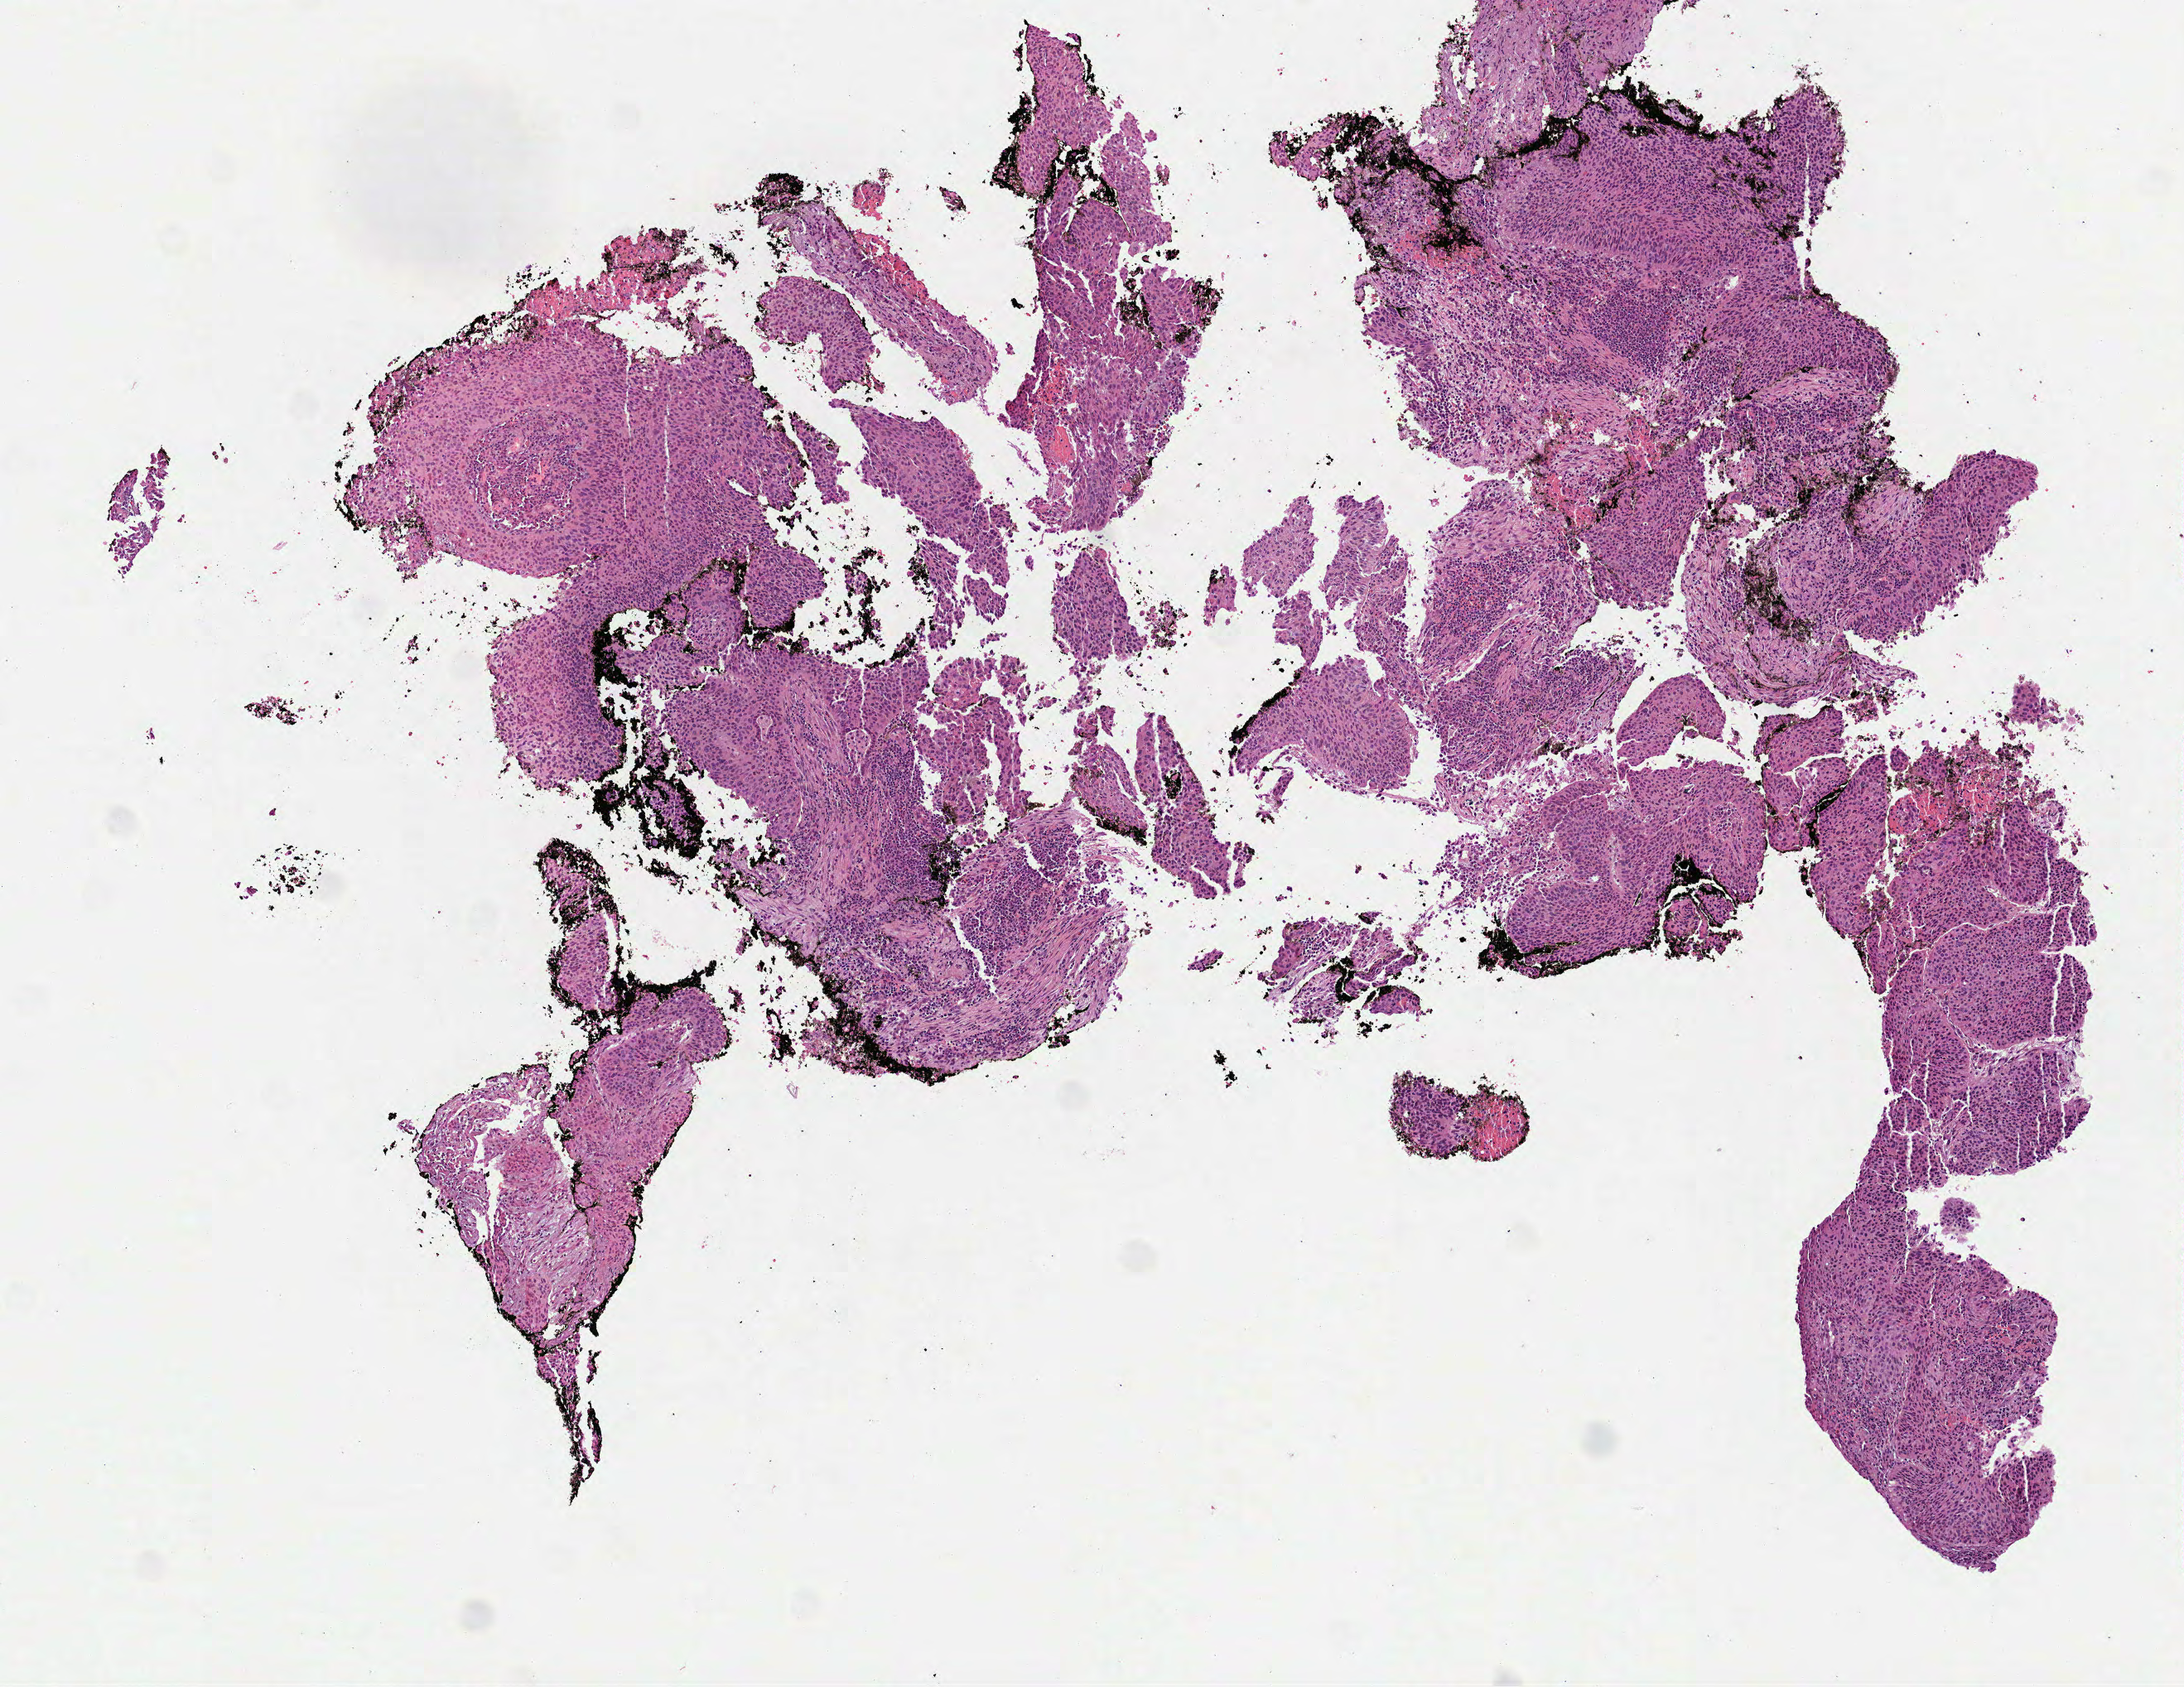
Digitized H&E tissue section (whole slide) — shown as a low-resolution overview of the whole scanned area (about 5.3 x 4.1 mm, from a 40x scan); formalin-fixed paraffin-embedded (FFPE) diagnostic section; lung, primary tumour sample. Patient: female, age at initial diagnosis 80 years.
Diagnosis: Squamous cell carcinoma, NOS (lower lobe, lung). TNM: T2b N0 MX. AJCC pathologic stage: IIA (7th edition). Laterality: right.